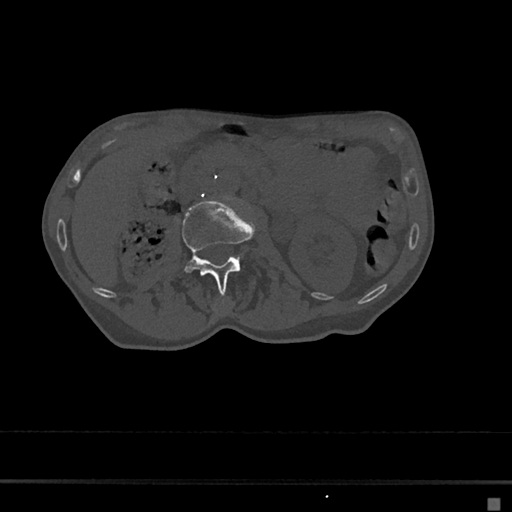
CT including the spine, one axial slice; position 9 of 797 along the scan axis; reconstruction kernel Br40s/3; bone window (W 1800 / L 400 HU); 0.5 mm slice thickness; 512 × 512 image matrix, field of view 360 × 360 mm. Patient: female, 68 years. Case-level facts recorded for this patient, not image findings: primary cancer: renal.
Outlined on this slice (semi-automatic segmentation, software-assisted and operator-edited):
- L2 vertebra: bounding box [x1, y1, x2, y2] px = [181, 199, 257, 293]